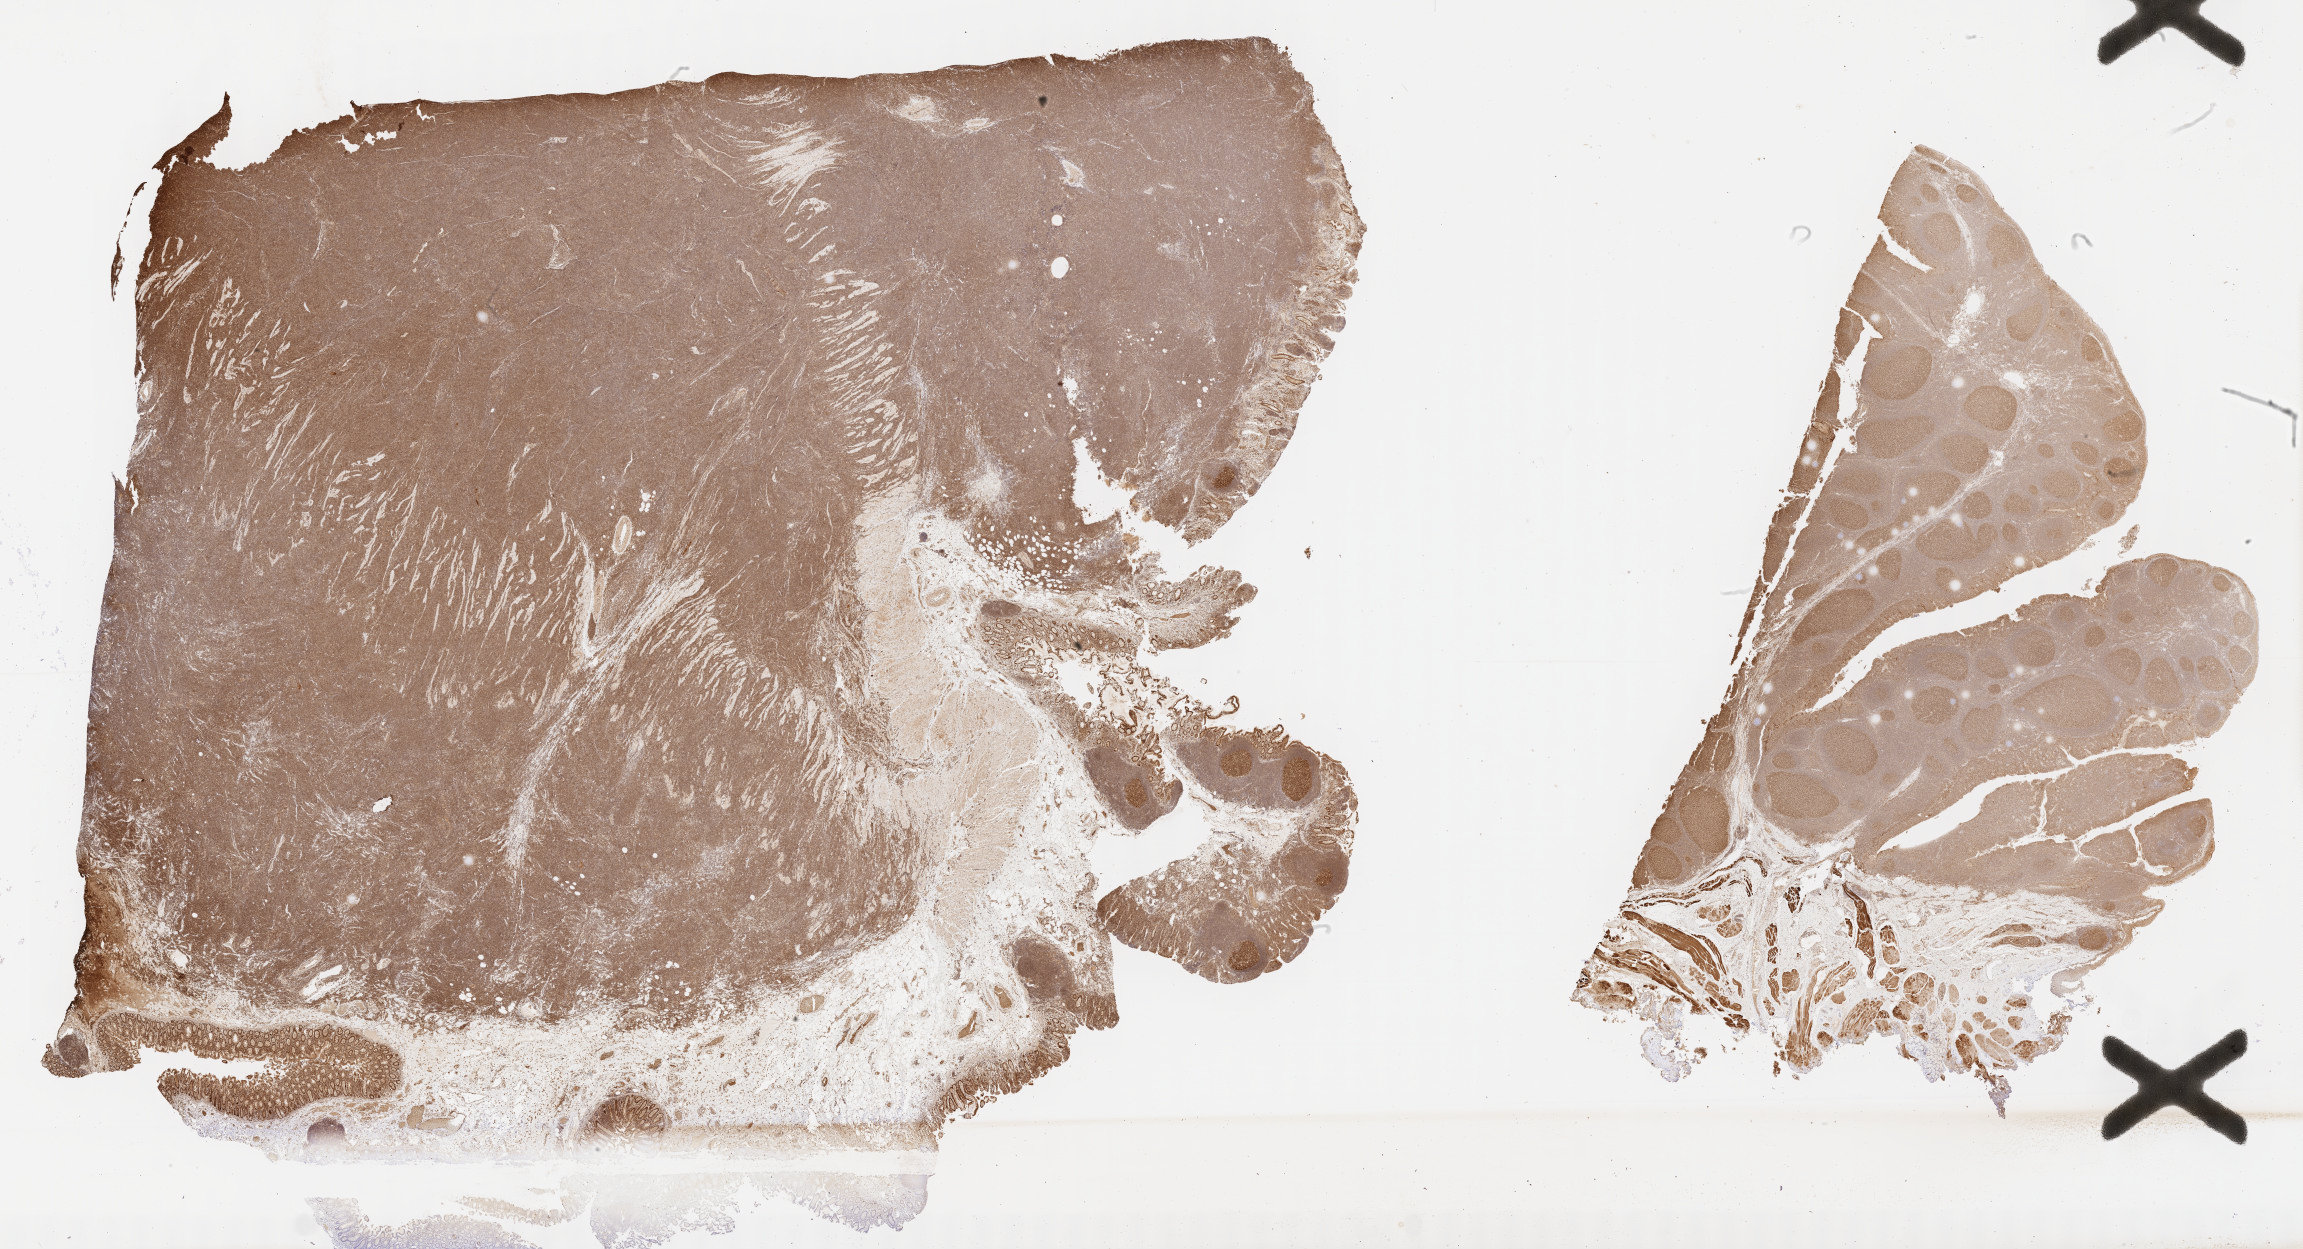
IHC for BCL6, whole-slide image, whole scanned area (about 37.2 x 20.2 mm) shown as a low-resolution overview; tumor tissue. Male patient, 59 years old.
Histologic diagnosis: Burkitt lymphoma, NOS.